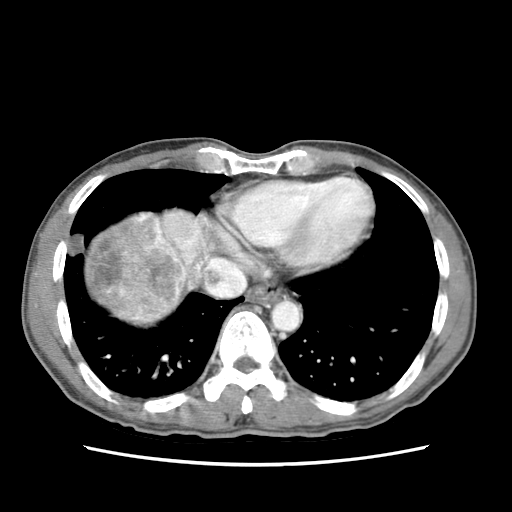
Contrast-enhanced abdominal CT (liver protocol), one axial slice; position 69 of 79 along the scan axis; 120 kVp; soft-tissue window (W 400 / L 40 HU); 512 × 512 image matrix, field of view 320 × 320 mm. From the clinical record (not read from this slice): diagnosis: hepatocellular carcinoma (patient treated with transarterial chemoembolisation; whether this scan precedes or follows treatment is not stated here); TNM stage (as recorded): Stage-IIIB; Child-Pugh class: A; tumour nodularity: multinodular.
Annotated regions visible in this slice (semi-automatic segmentation, software-assisted and operator-edited):
- liver parenchyma outside the tumour (the mass and vessels are separate outlines, so this box may not span the whole liver): bounding box (x1, y1, x2, y2) in pixels: (84, 206, 218, 324)
- mass: (87, 212, 189, 322)
- liver vessels: (156, 209, 199, 258)